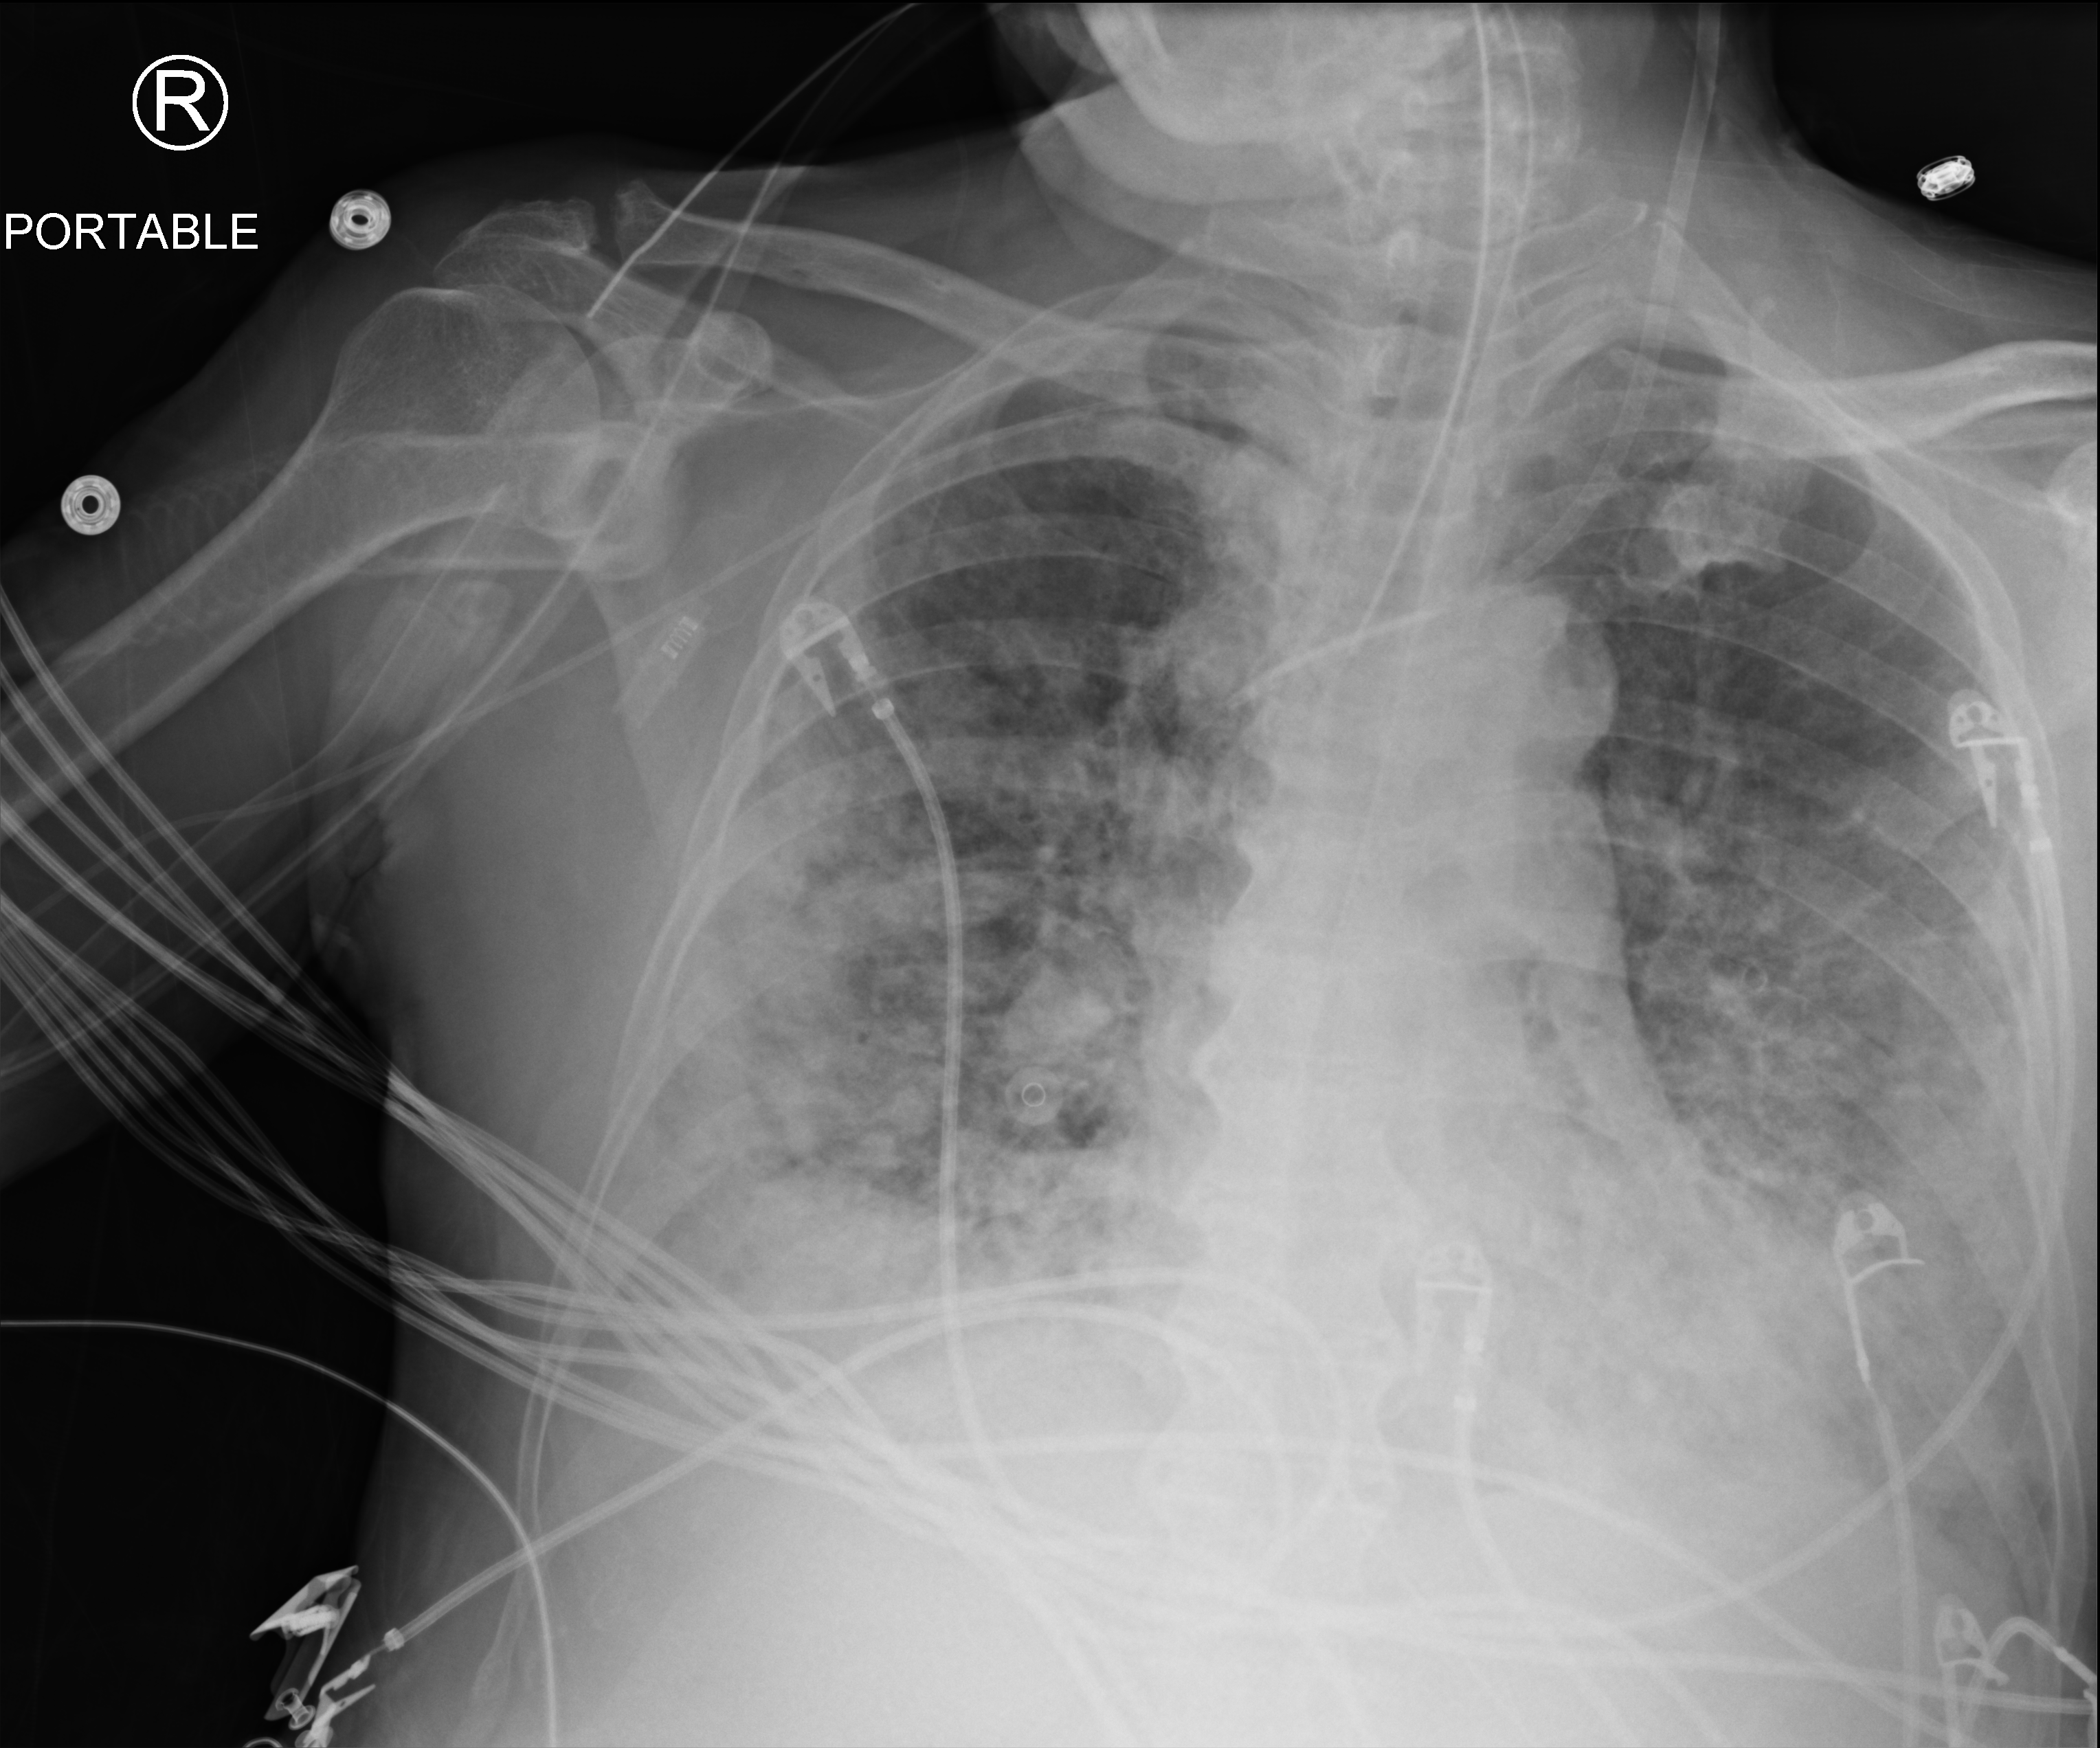
Chest X-ray (portable), anteroposterior (AP) projection. Male patient hospitalised with COVID-19, age 60–74 years.
From the hospital-stay record, not from the radiograph (when in the stay this image was taken is not recorded):
- length of hospital stay: 26 days
- mechanically ventilated during this hospital stay: yes